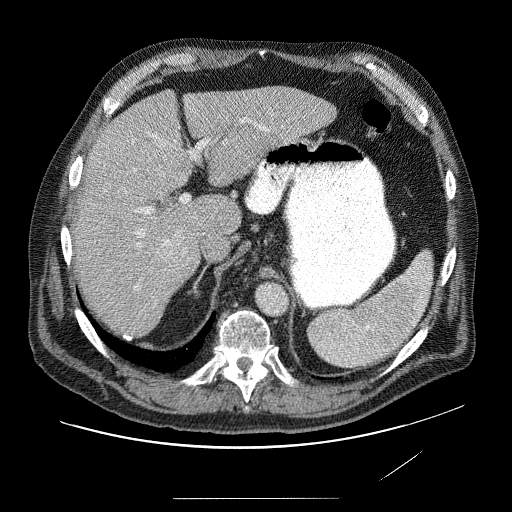
Contrast-enhanced abdominal CT (liver protocol), one axial slice. Slice 53 of 89 in the series (ordered by position). Soft-tissue window (W 400 / L 40 HU). 2.5 mm slice thickness. 512 × 512 image matrix, field of view 420 × 420 mm. Case-level facts recorded for this patient, not image findings: diagnosis: hepatocellular carcinoma (patient treated with transarterial chemoembolisation; whether this scan precedes or follows treatment is not stated here); TNM stage (as recorded): Stage-IVA; Child-Pugh class: A; tumour differentiation: moderately differentiated; tumour nodularity: multinodular.
Annotated regions visible in this slice (semi-automatic segmentation, software-assisted and operator-edited):
- abdominal aorta: box from (x=256, y=283) to (x=286, y=314) px
- liver parenchyma outside the tumour (the mass and vessels are separate outlines, so this box may not span the whole liver): (x=74, y=86)–(x=340, y=324)
- mass: (x=139, y=128)–(x=194, y=183)
- liver vessels: (x=125, y=127)–(x=298, y=296)